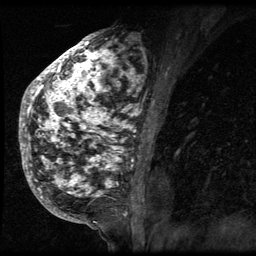
Breast MRI (dynamic contrast-enhanced), one sagittal slice. 3 images stored at this slice position (order not interpretable as contrast timing). 1.5 T. TE 4.2 ms, TR 9 ms. 2.5 mm slice thickness. 256 × 256 image matrix, field of view 180 × 180 mm. Patient: female, 50 years. Case-level facts recorded for this patient, not image findings: setting: breast cancer imaged before/during neoadjuvant chemotherapy; receptor status: triple-negative.
Structures marked on this image (semi-automatic segmentation, software-assisted and operator-edited):
- analysis volume of interest (the breast-tissue region the enhancement analysis was run in; not a lesion): bounding box (x1, y1, x2, y2) in pixels: (24, 39, 140, 212)
- tumour enhancement mask (voxels above the 140 % enhancement threshold inside the analysis volume of interest): (24, 39, 140, 210)